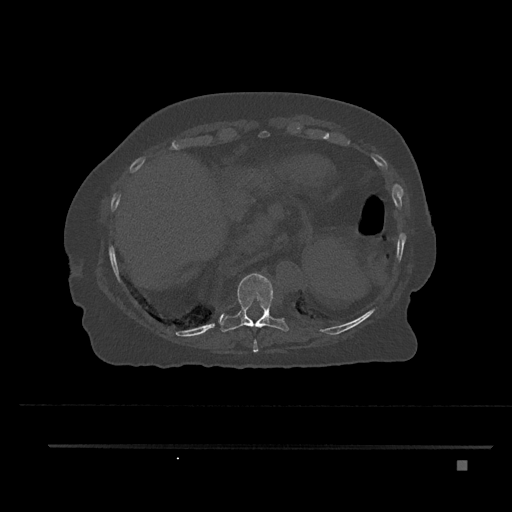
CT including the spine, one axial slice; position 359 of 797 along the scan axis; bone window (W 1800 / L 400 HU); 0.5 mm slice thickness; 512 × 512 image matrix. Patient: female, 76 years. Case-level facts recorded for this patient, not image findings: primary cancer: lung.
Annotated regions visible in this slice (semi-automatically segmented with operator editing):
- T10 vertebra: bounding box <220,273,289,332> (left, top, right, bottom; pixels)
- T9 vertebra: <253,339,259,353>